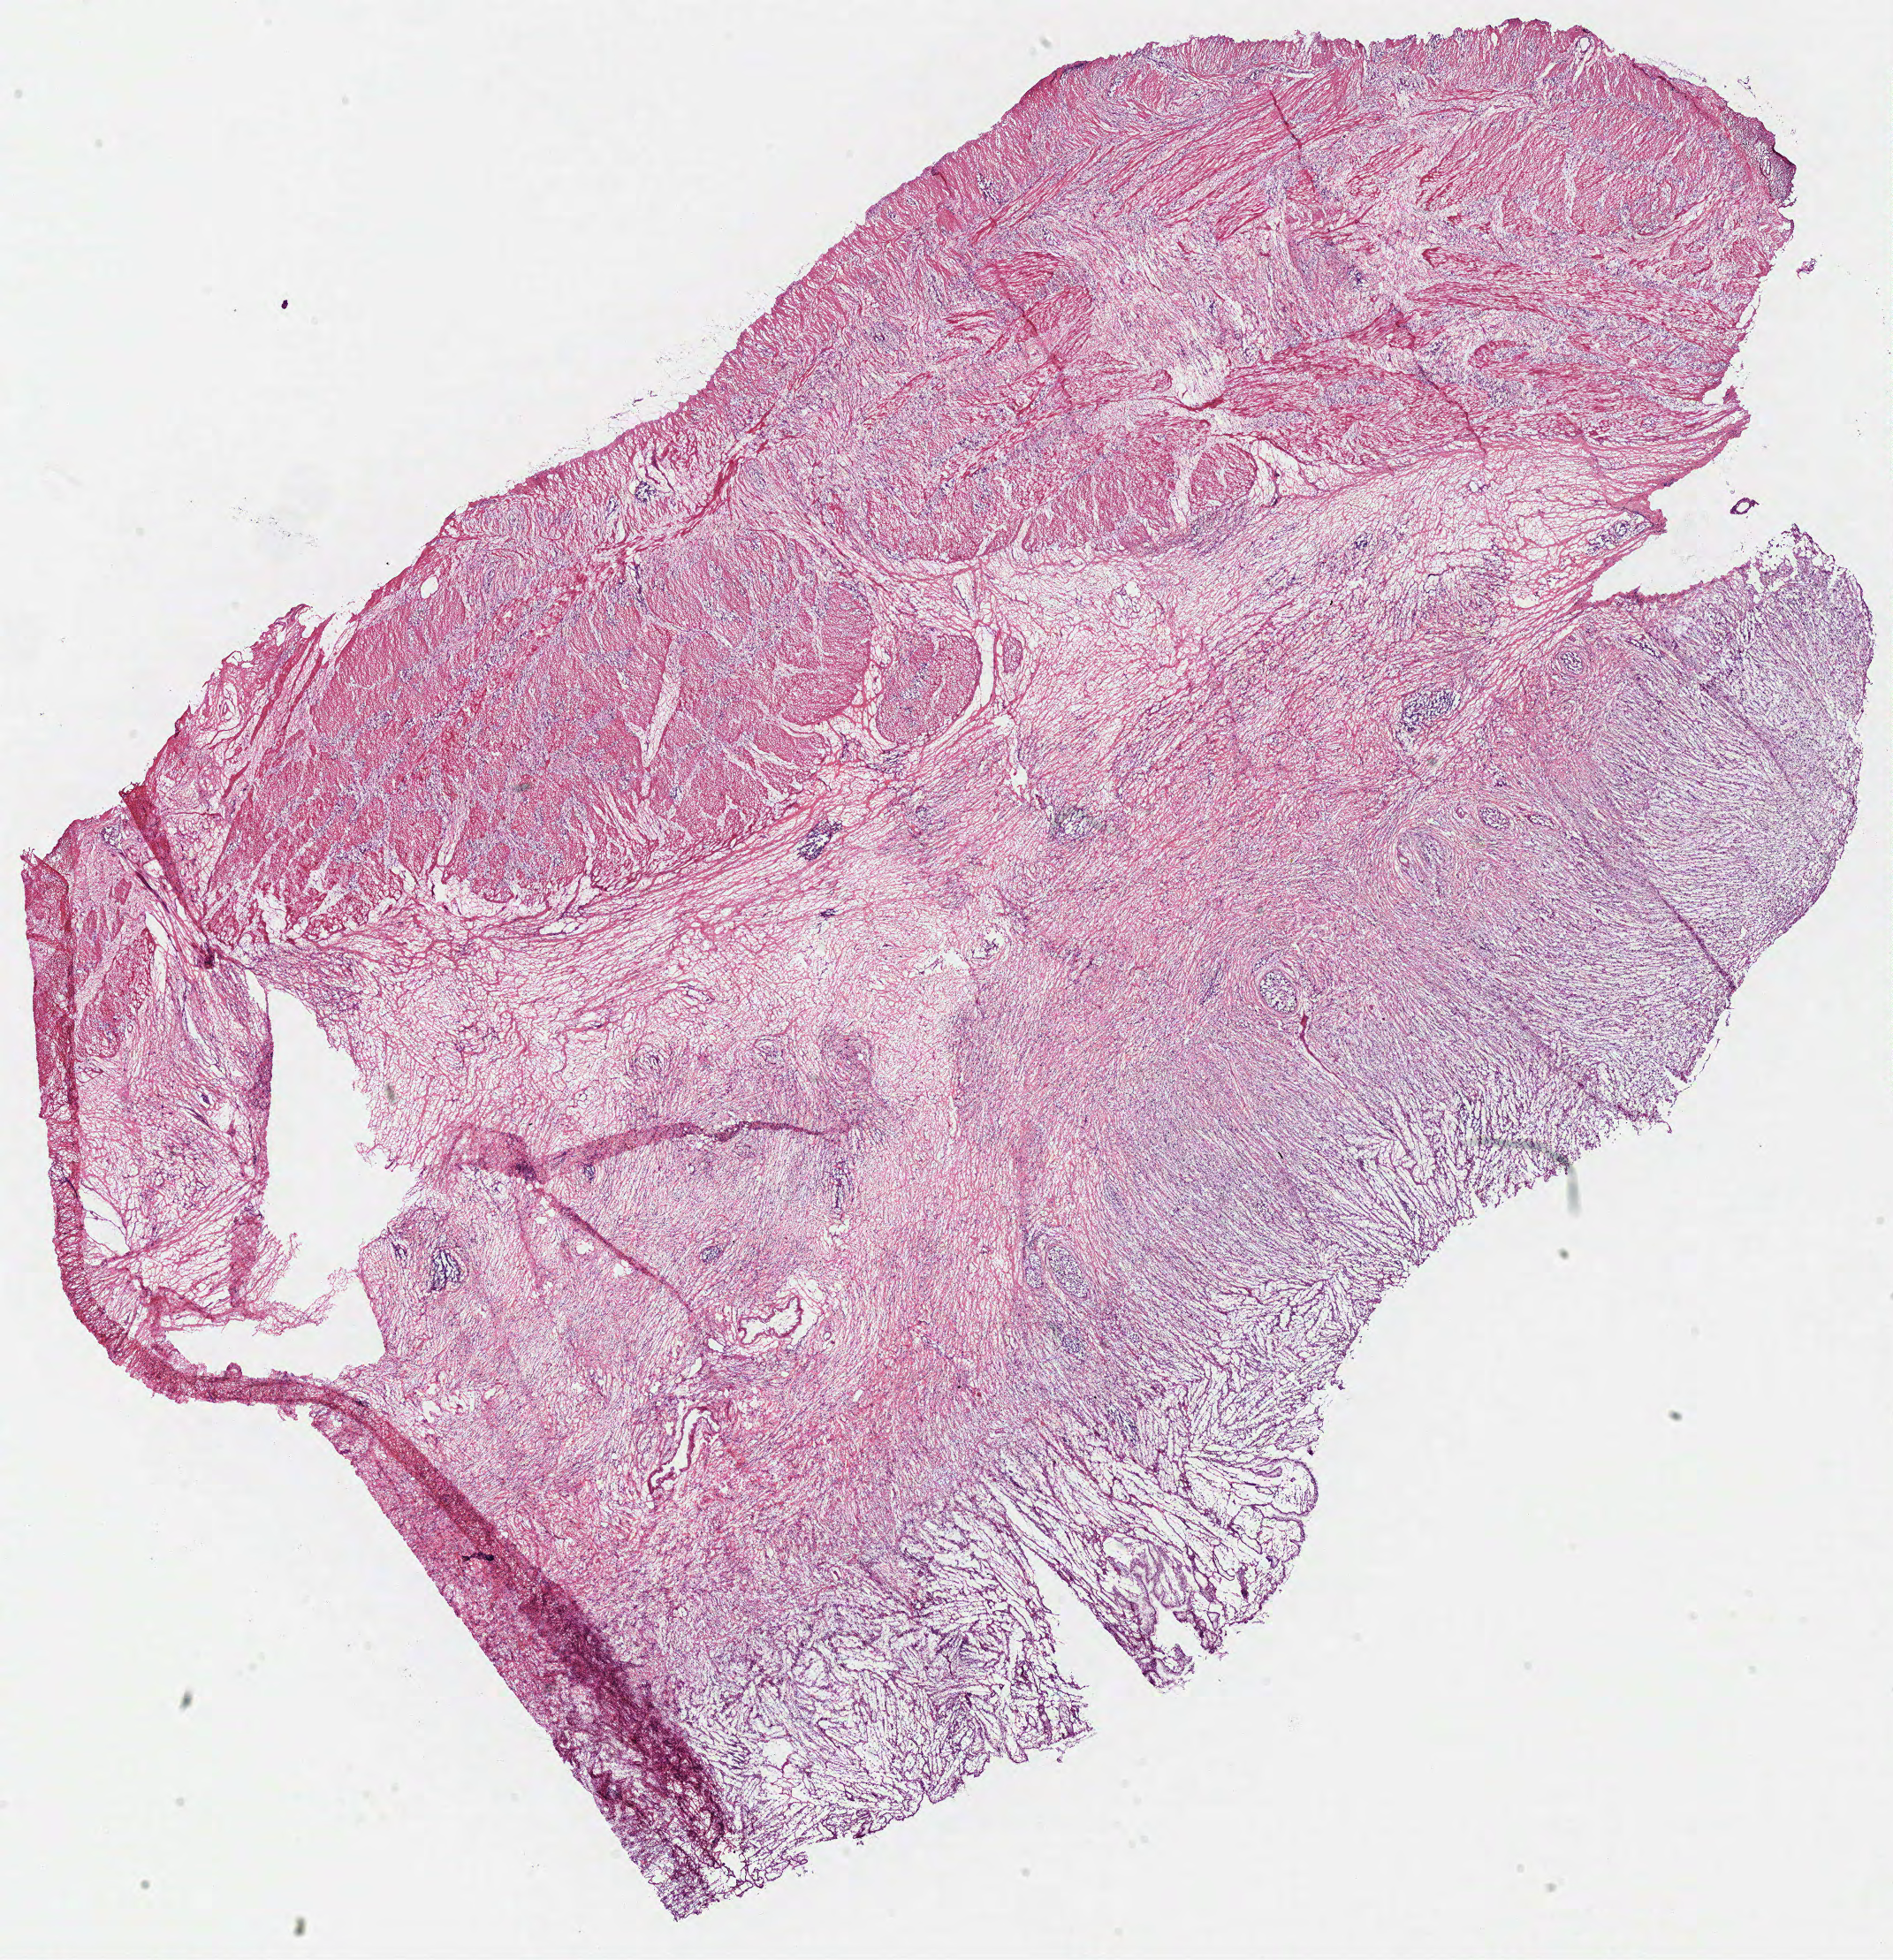
Whole-slide histology image, Hematoxylin and eosin (H&E) stained, low-resolution overview of the scanned area, about 16.9 x 17.5 mm (from a 40x scan). Frozen section. Sample: primary tumour, stomach. Female, age 54 years at initial diagnosis. Histologic grade: G3 (poorly differentiated). Composition of this section per pathologist review: tumour cells 65%, tumour nuclei 65%, normal cells 0%, stromal cells 35%, necrosis 0%.
Lymph nodes positive (case pathology): 0 of 5 examined. AJCC pathologic stage: IIA (7th edition). Histologic diagnosis: Carcinoma, diffuse type.